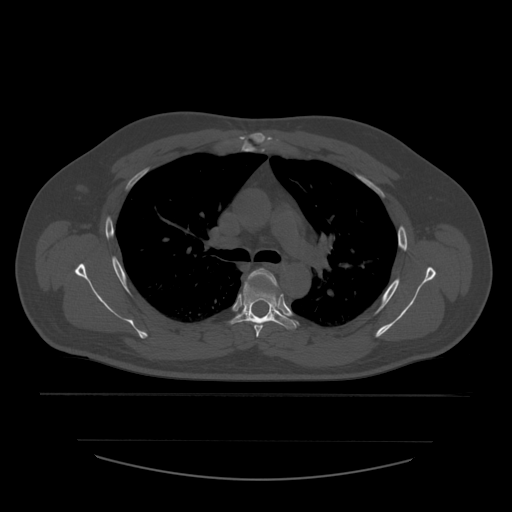
CT including the spine, one axial slice. Position 404 of 532 along the scan axis. Reconstruction kernel STANDARD. 120 kVp. Bone window (W 1800 / L 400 HU). 512 × 512 image matrix, field of view 441 × 441 mm. Patient age 44 years. Case-level facts recorded for this patient, not image findings: primary cancer: soft tissue sarcoma.
Structures marked on this image (semi-automatically segmented with operator editing):
- T4 vertebra: bounding box [x1, y1, x2, y2] px = [249, 269, 277, 338]
- T5 vertebra: [230, 280, 297, 329]